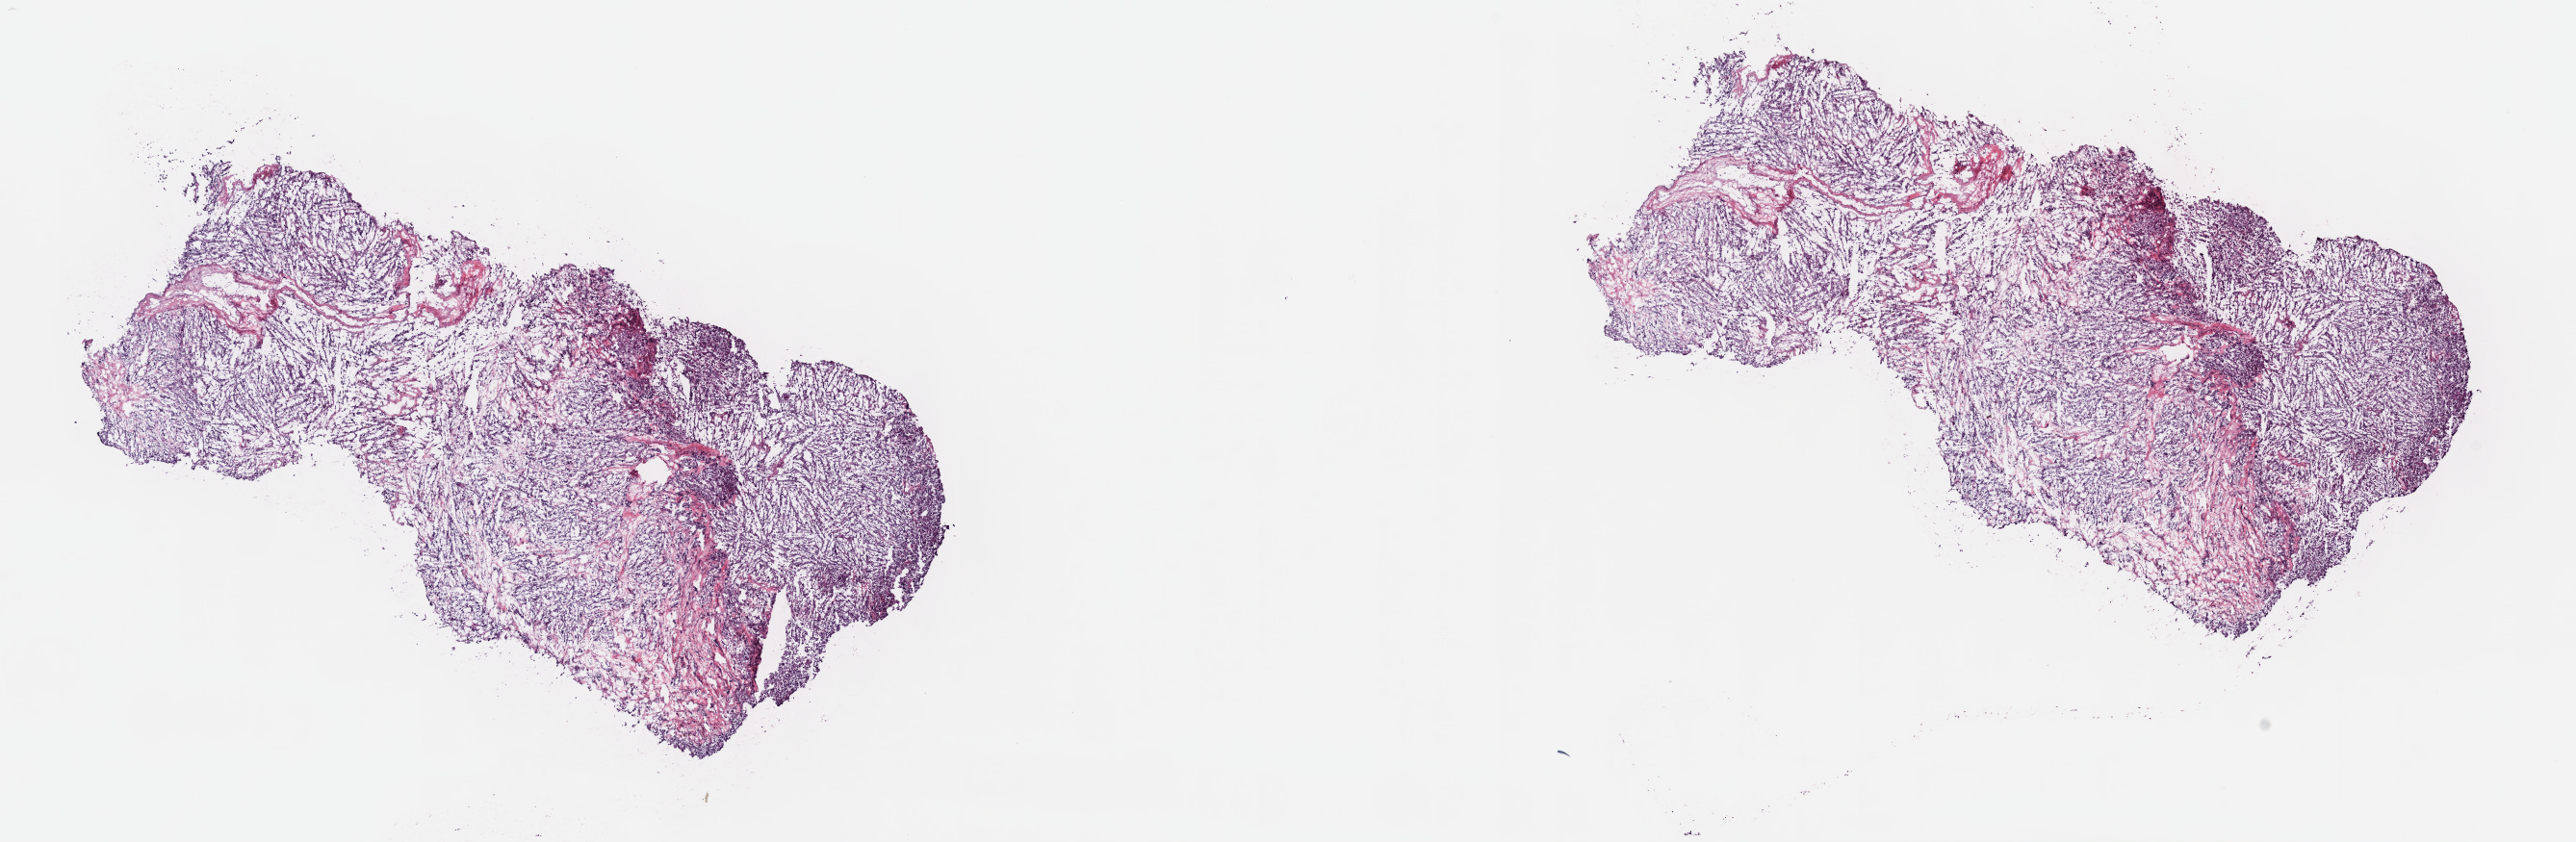
Digitized H&E-stained tissue section (whole slide), low-resolution overview of the scanned area, about 21.6 x 7.1 mm. Frozen section from the top of the tissue portion. Adrenal gland, primary tumour sample. Patient: female, age at initial diagnosis 44 years. Pathologist review of this section (percent, as recorded): tumour cells 100%, tumour nuclei 80%, normal cells 0%, stromal cells 0%, necrosis 0%. Inflammatory infiltration, as recorded: lymphocyte infiltration 2%, monocyte infiltration 0%, neutrophil infiltration 0%.
Histologic diagnosis: Pheochromocytoma, NOS.